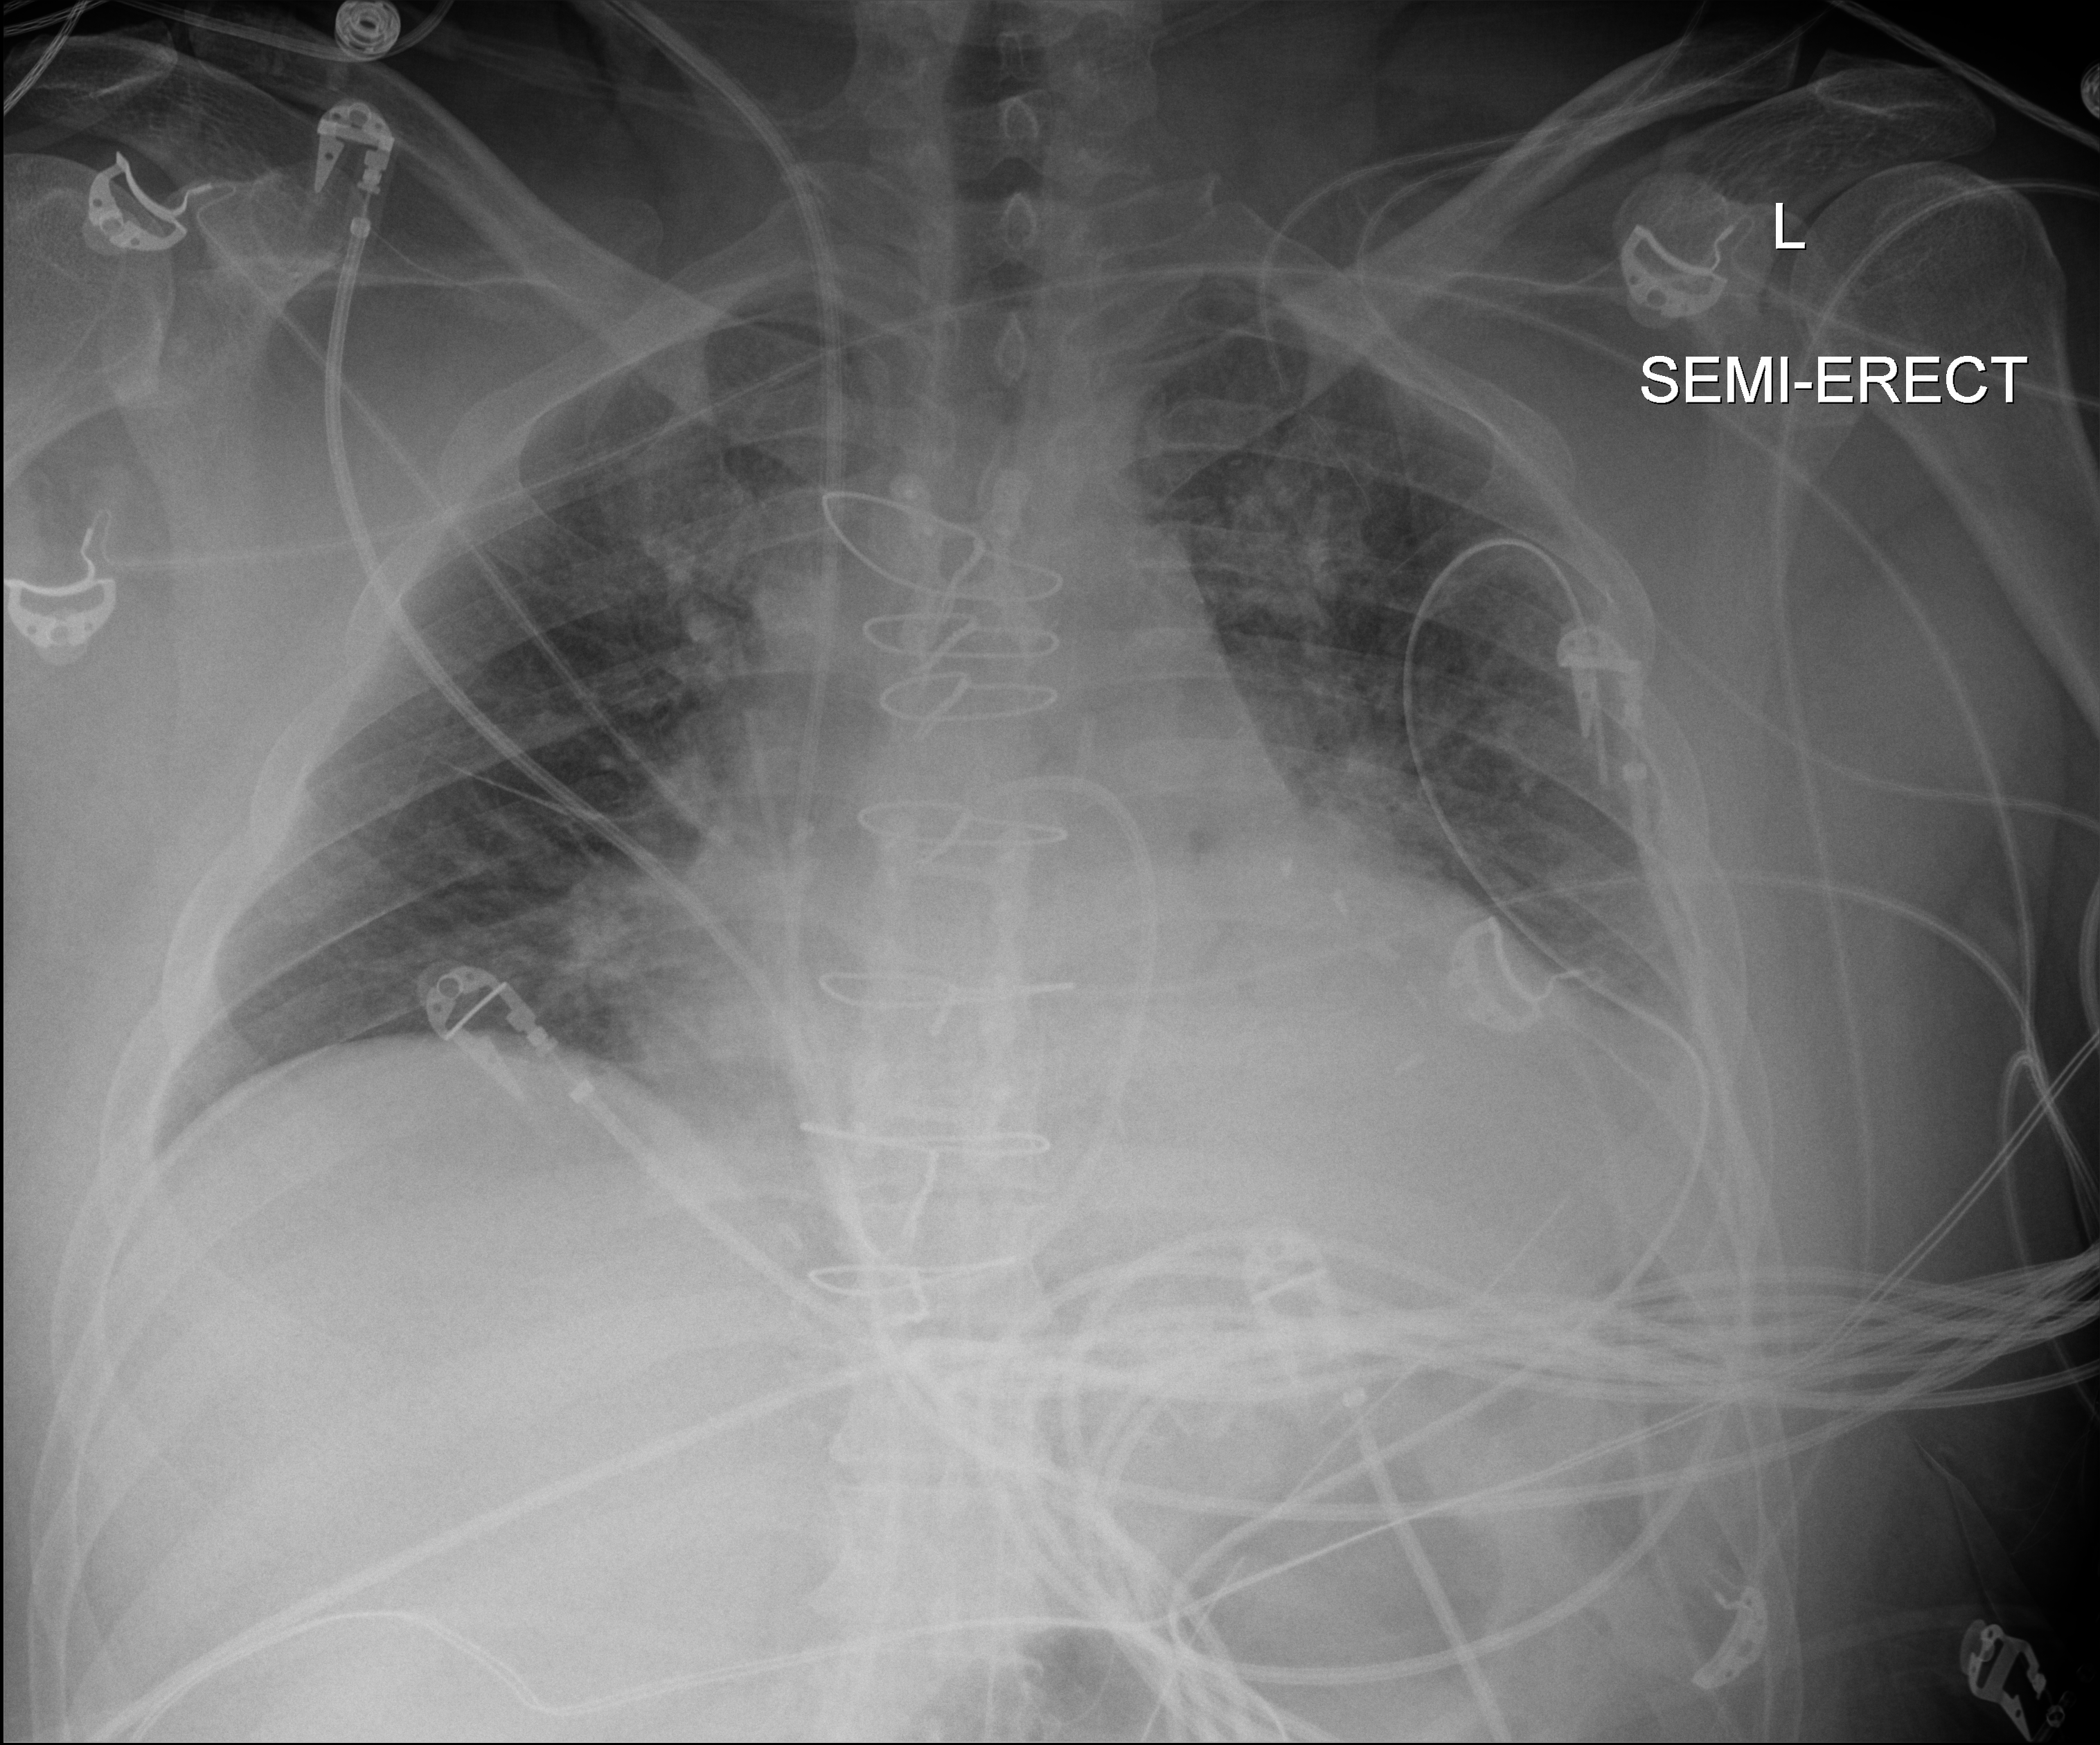
Portable chest radiograph, anteroposterior (AP) projection. Male patient hospitalised with COVID-19, age 18–59 years.
Hospital-stay facts (about this admission, not read from this image; timing relative to this image not recorded):
- admitted to intensive care during this hospital stay: no